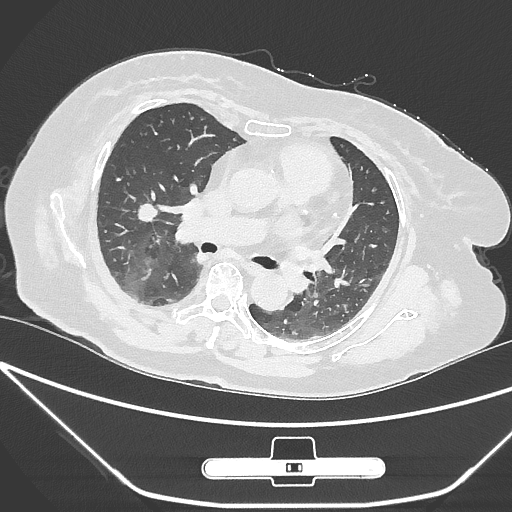
Chest CT, one axial slice; slice 155 of 245 in the series (ordered by position); lung window (W 1500 / L -600 HU); 1 mm slice thickness; 512 × 512 image matrix, field of view 365 × 365 mm. Female patient, age 65 years. Case-level facts recorded for this patient, not image findings: clinical TNM (as recorded): T1c N0 M0; histopathological grade: G3.
Annotated regions visible in this slice (rectangle marked by the reading radiologist):
- lung tumour (recorded histology: adenocarcinoma): box from (x=128, y=192) to (x=161, y=225) px